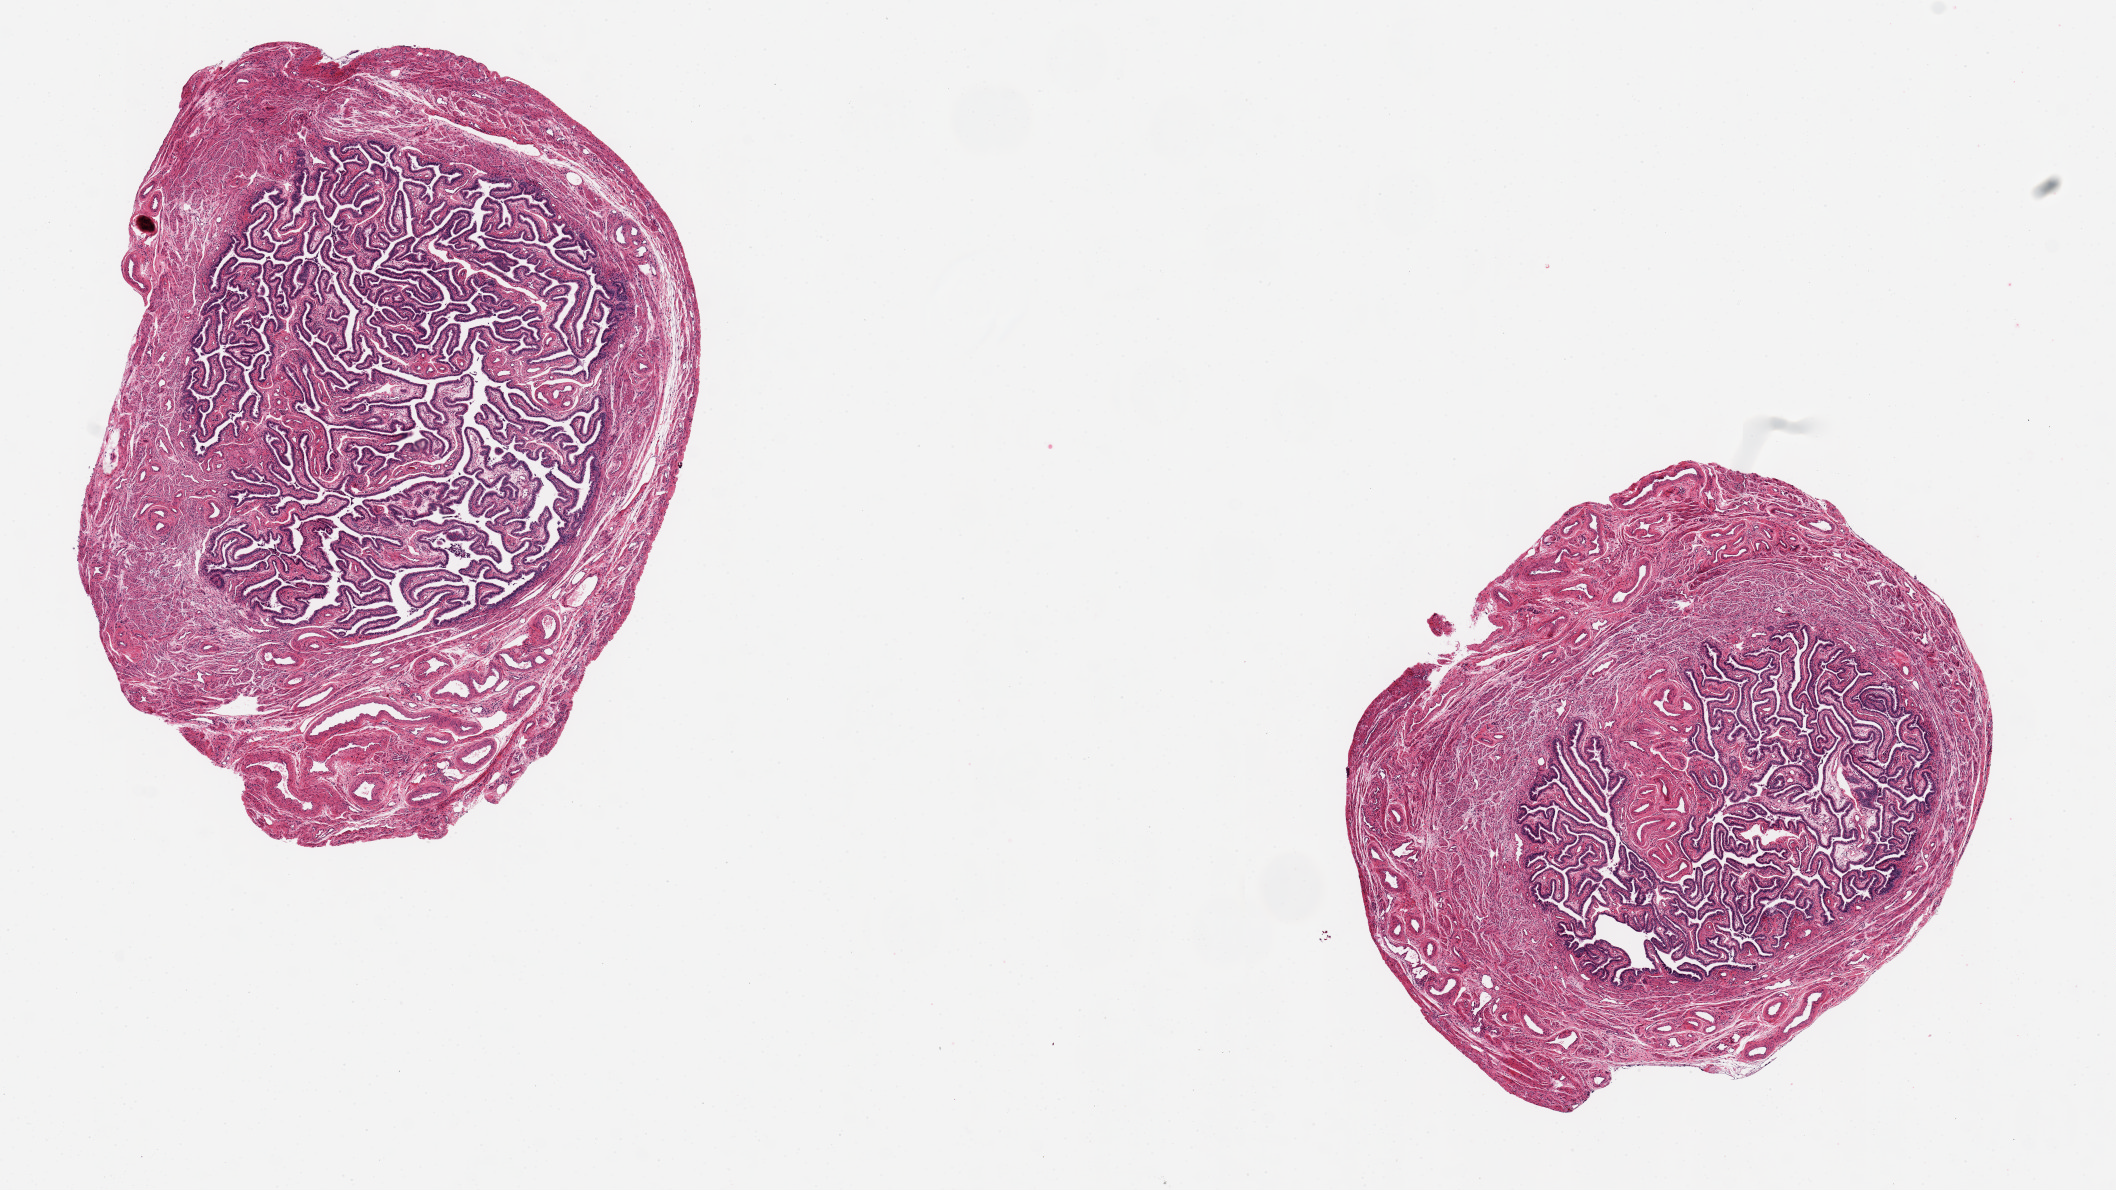
Digitized H&E-stained section — whole scanned area (about 16.7 x 9.4 mm) shown as a low-resolution overview; PAXgene-fixed, paraffin-embedded tissue; target tissue: fallopian tube; tissue donor sample. Donor: female.
* review note (as recorded): 2 aliquots, ~5.5mm. Excellent preservation of tubal epithelium